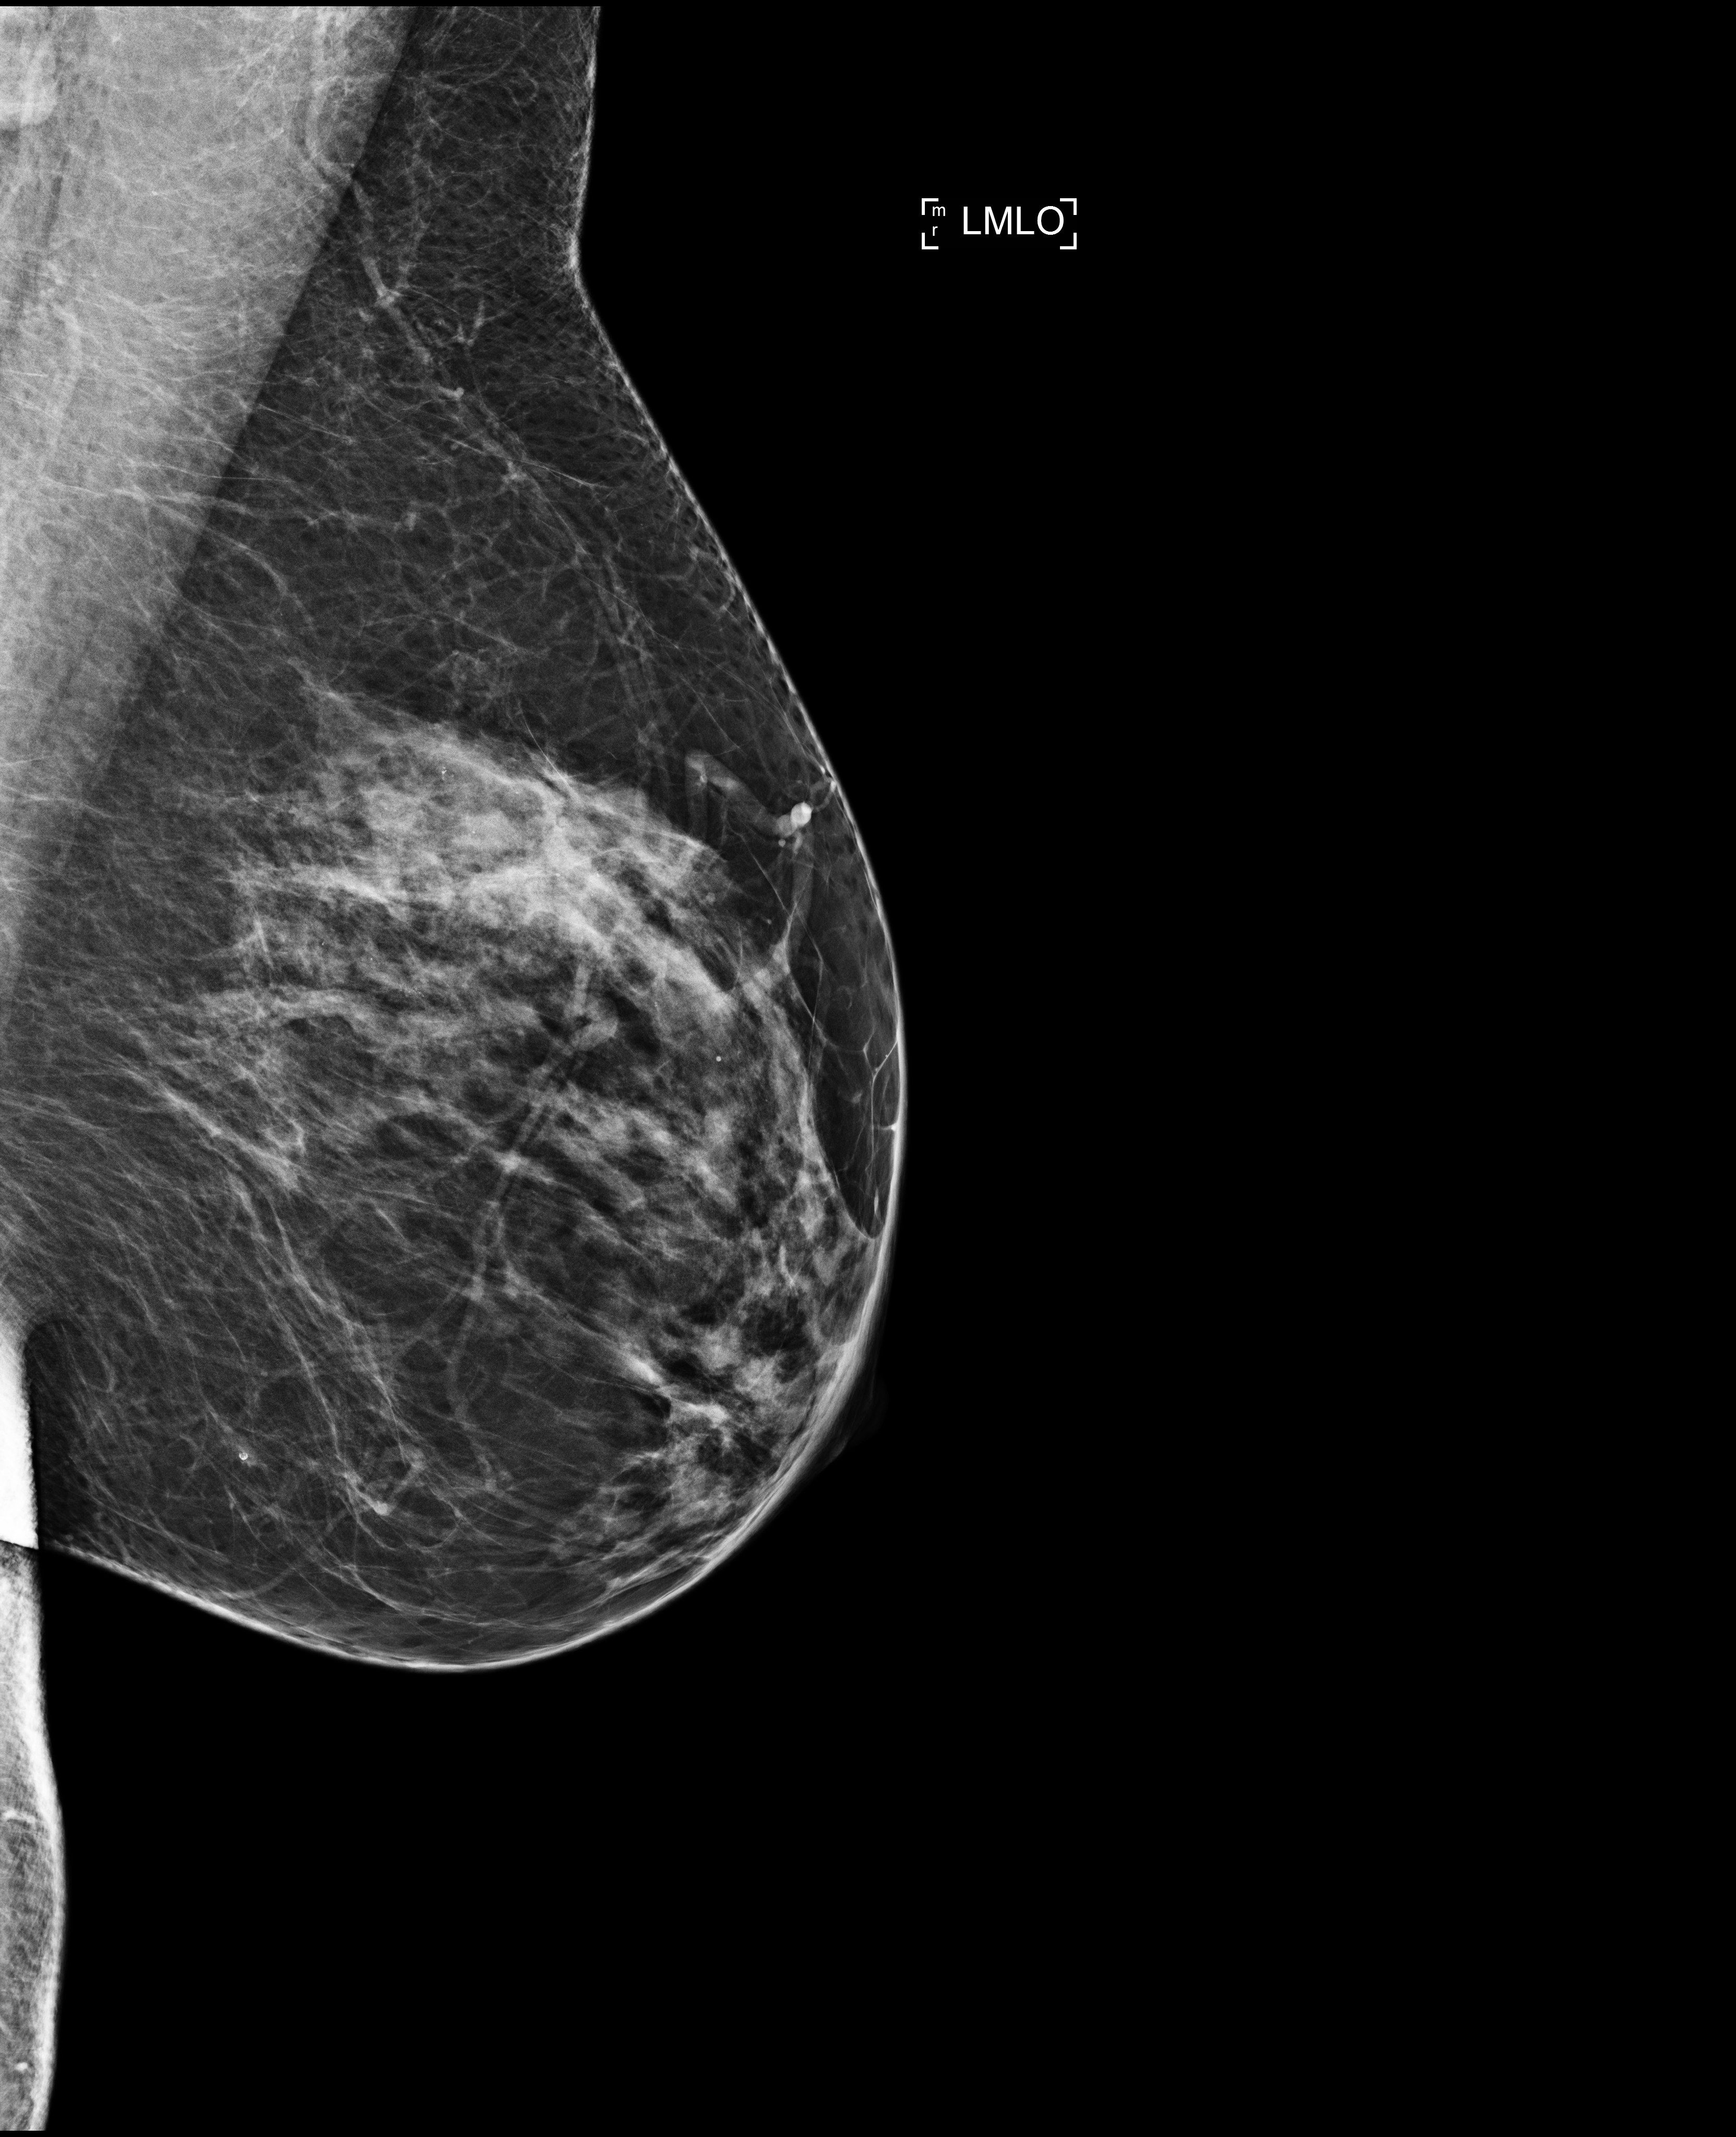
Annual screening mammography examination, compressed breast thickness 71 mm. Female patient, age 60 years.
Image type: full-field digital mammogram. Breast: left. Projection: MLO view.